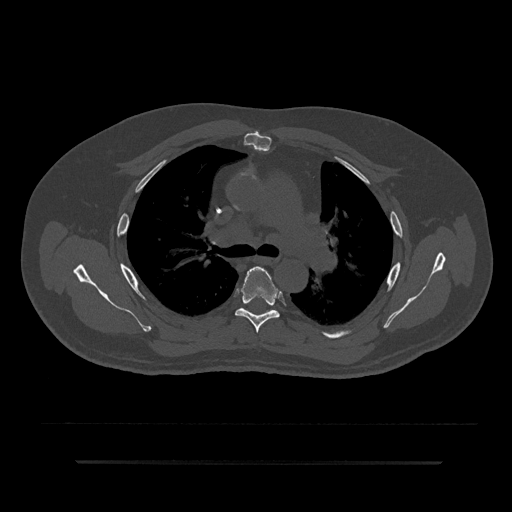
CT including the spine, one axial slice; position 573 of 797 along the scan axis; reconstruction kernel Br40s/3; 120 kVp; bone window (W 1800 / L 400 HU); 0.5 mm slice thickness; 512 × 512 image matrix, field of view 464 × 464 mm. Patient: male, 59 years. Case-level facts recorded for this patient, not image findings: primary cancer: bile ducts; vertebrae with lytic lesions (as recorded): T10.
Annotated regions visible in this slice (semi-automatically segmented with operator editing):
- T5 vertebra: bounding box [x1, y1, x2, y2] px = [235, 266, 280, 333]
- T6 vertebra: [245, 309, 247, 311]